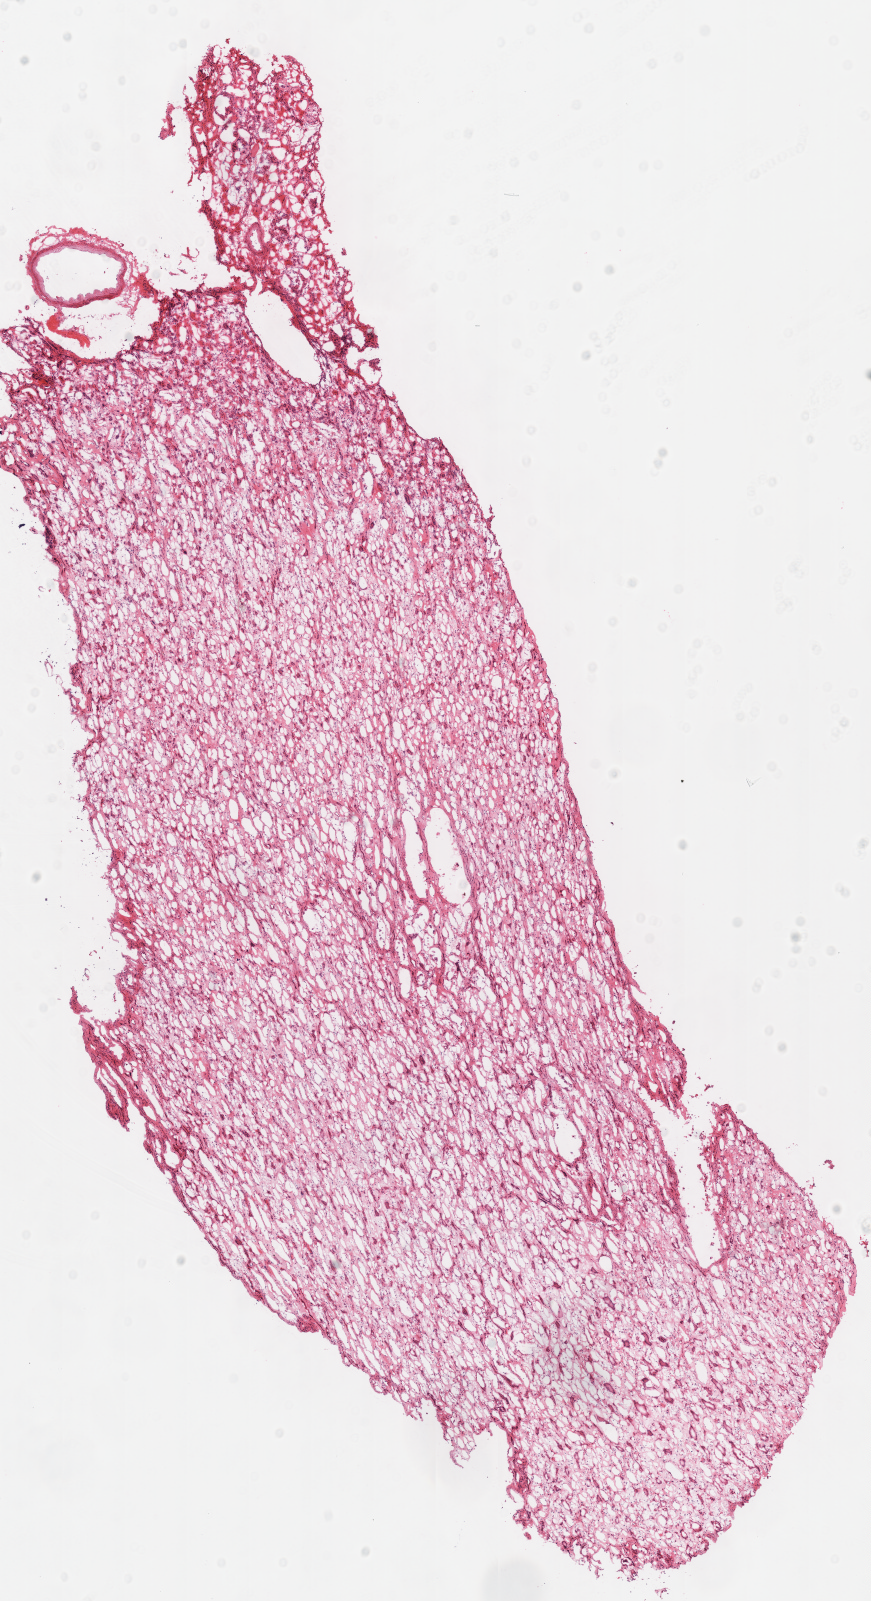
Digitized H&E-stained tissue section (whole slide), whole scanned area (about 6.9 x 12.6 mm) shown as a low-resolution overview. Frozen section. Kidney, solid tissue normal (non-tumour tissue) sample. Patient: female, age at initial diagnosis 86 years. Infiltration values recorded for this section: lymphocyte infiltration 0%, monocyte infiltration 0%, neutrophil infiltration 0%.
* this section: solid tissue normal (non-tumour) sample from the same patient
* patient diagnosis: Renal cell carcinoma, chromophobe type